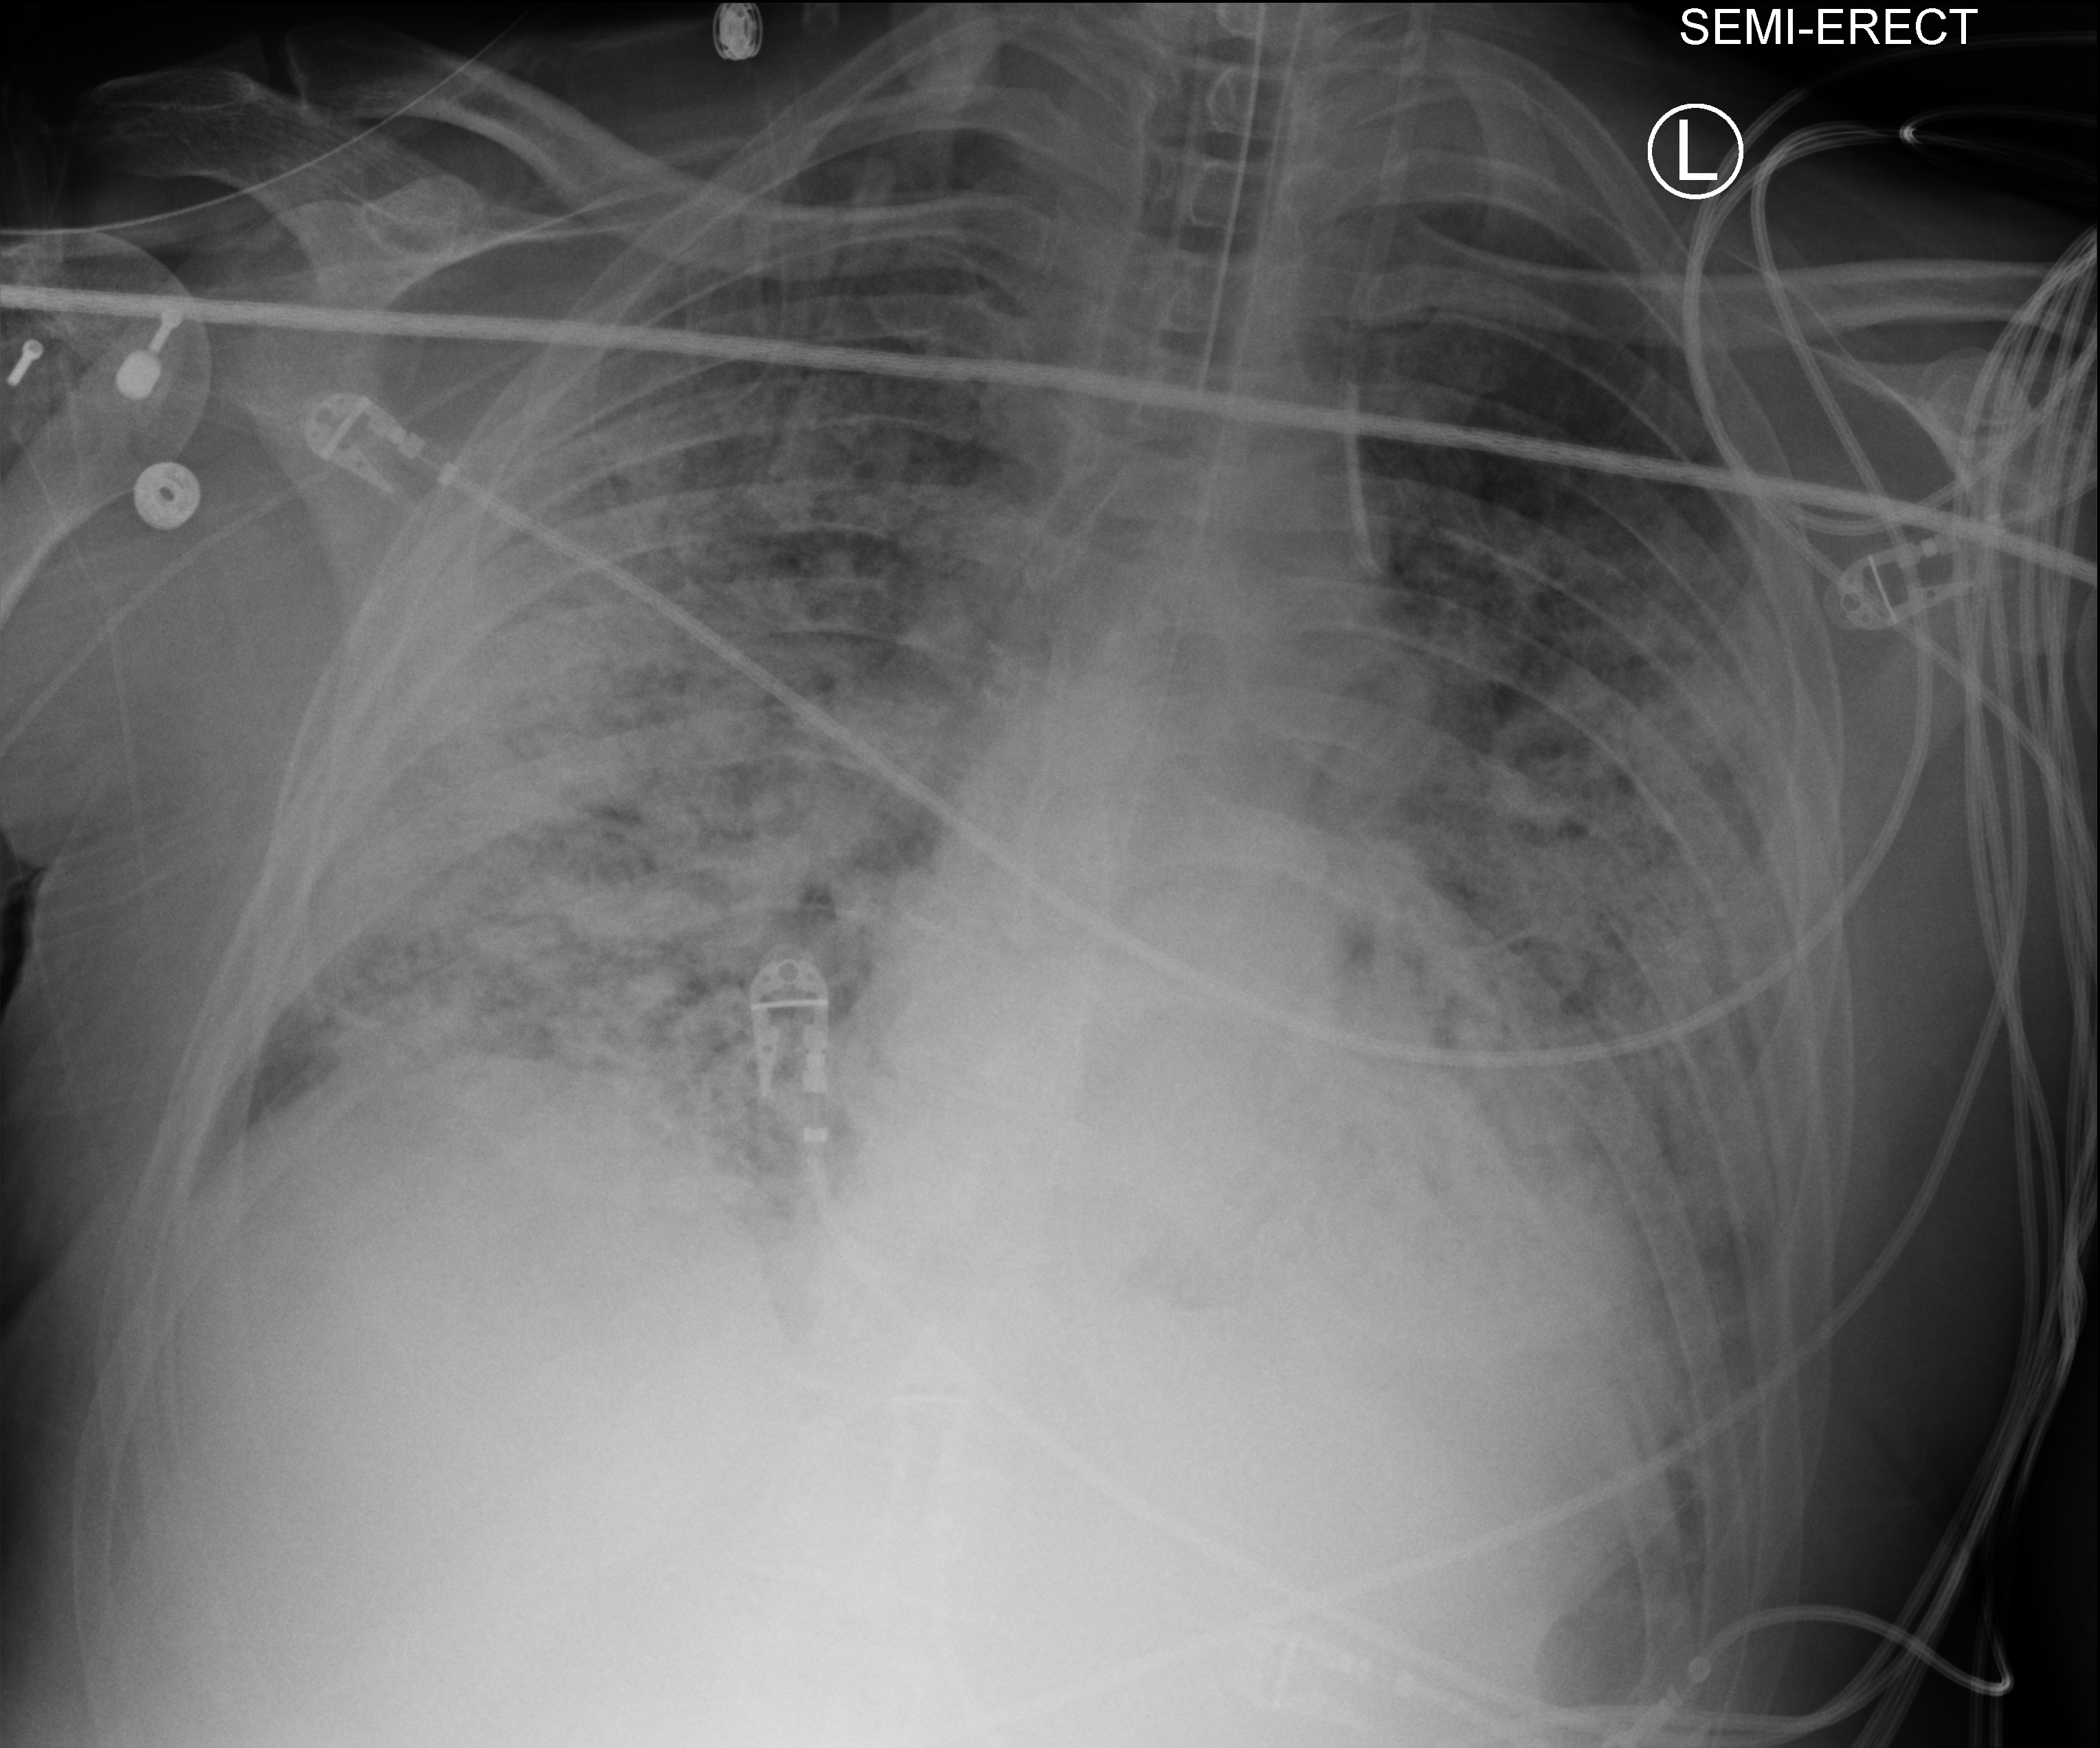
Chest X-ray (portable). Male patient hospitalised with COVID-19, age 18–59 years.
Hospital-stay facts (about this admission, not read from this image; timing relative to this image not recorded):
- admitted to intensive care during this hospital stay: yes
- mechanically ventilated during this hospital stay: yes
- chronic kidney disease (admission record): no